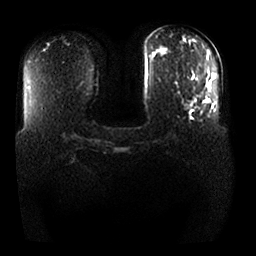
Breast MRI, one axial slice; position 10 of 25 along the scan axis; diffusion-weighted series; image 2 of 4 stored at this slice position (different b-values; order by instance number); 1.5 T; 256 × 256 image matrix, field of view 370 × 370 mm. Female patient.
Annotated regions visible in this slice (outlined manually by an expert reader):
- tumour on diffusion-weighted imaging: bounding box (x1, y1, x2, y2) in pixels: (183, 83, 211, 107)